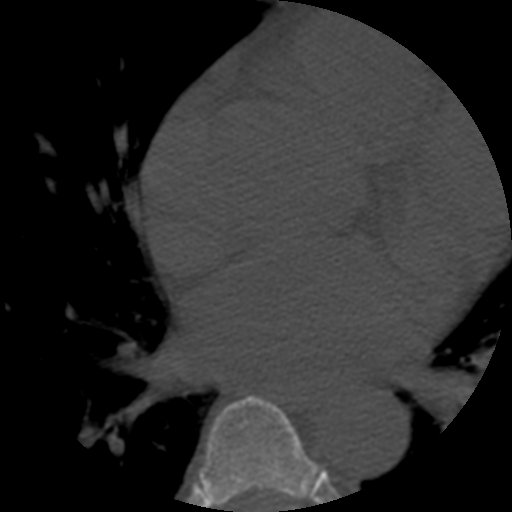
CT including the spine, one axial slice; slice 348 of 508 in the series (ordered by position); 120 kVp; bone window (W 1800 / L 400 HU); 1.25 mm slice thickness; 512 × 512 image matrix. Patient age 57 years. Case-level facts recorded for this patient, not image findings: primary cancer: prostate.
Structures marked on this image (semi-automatically segmented with operator editing):
- T6 vertebra: bounding box <198,395,322,512> (left, top, right, bottom; pixels)